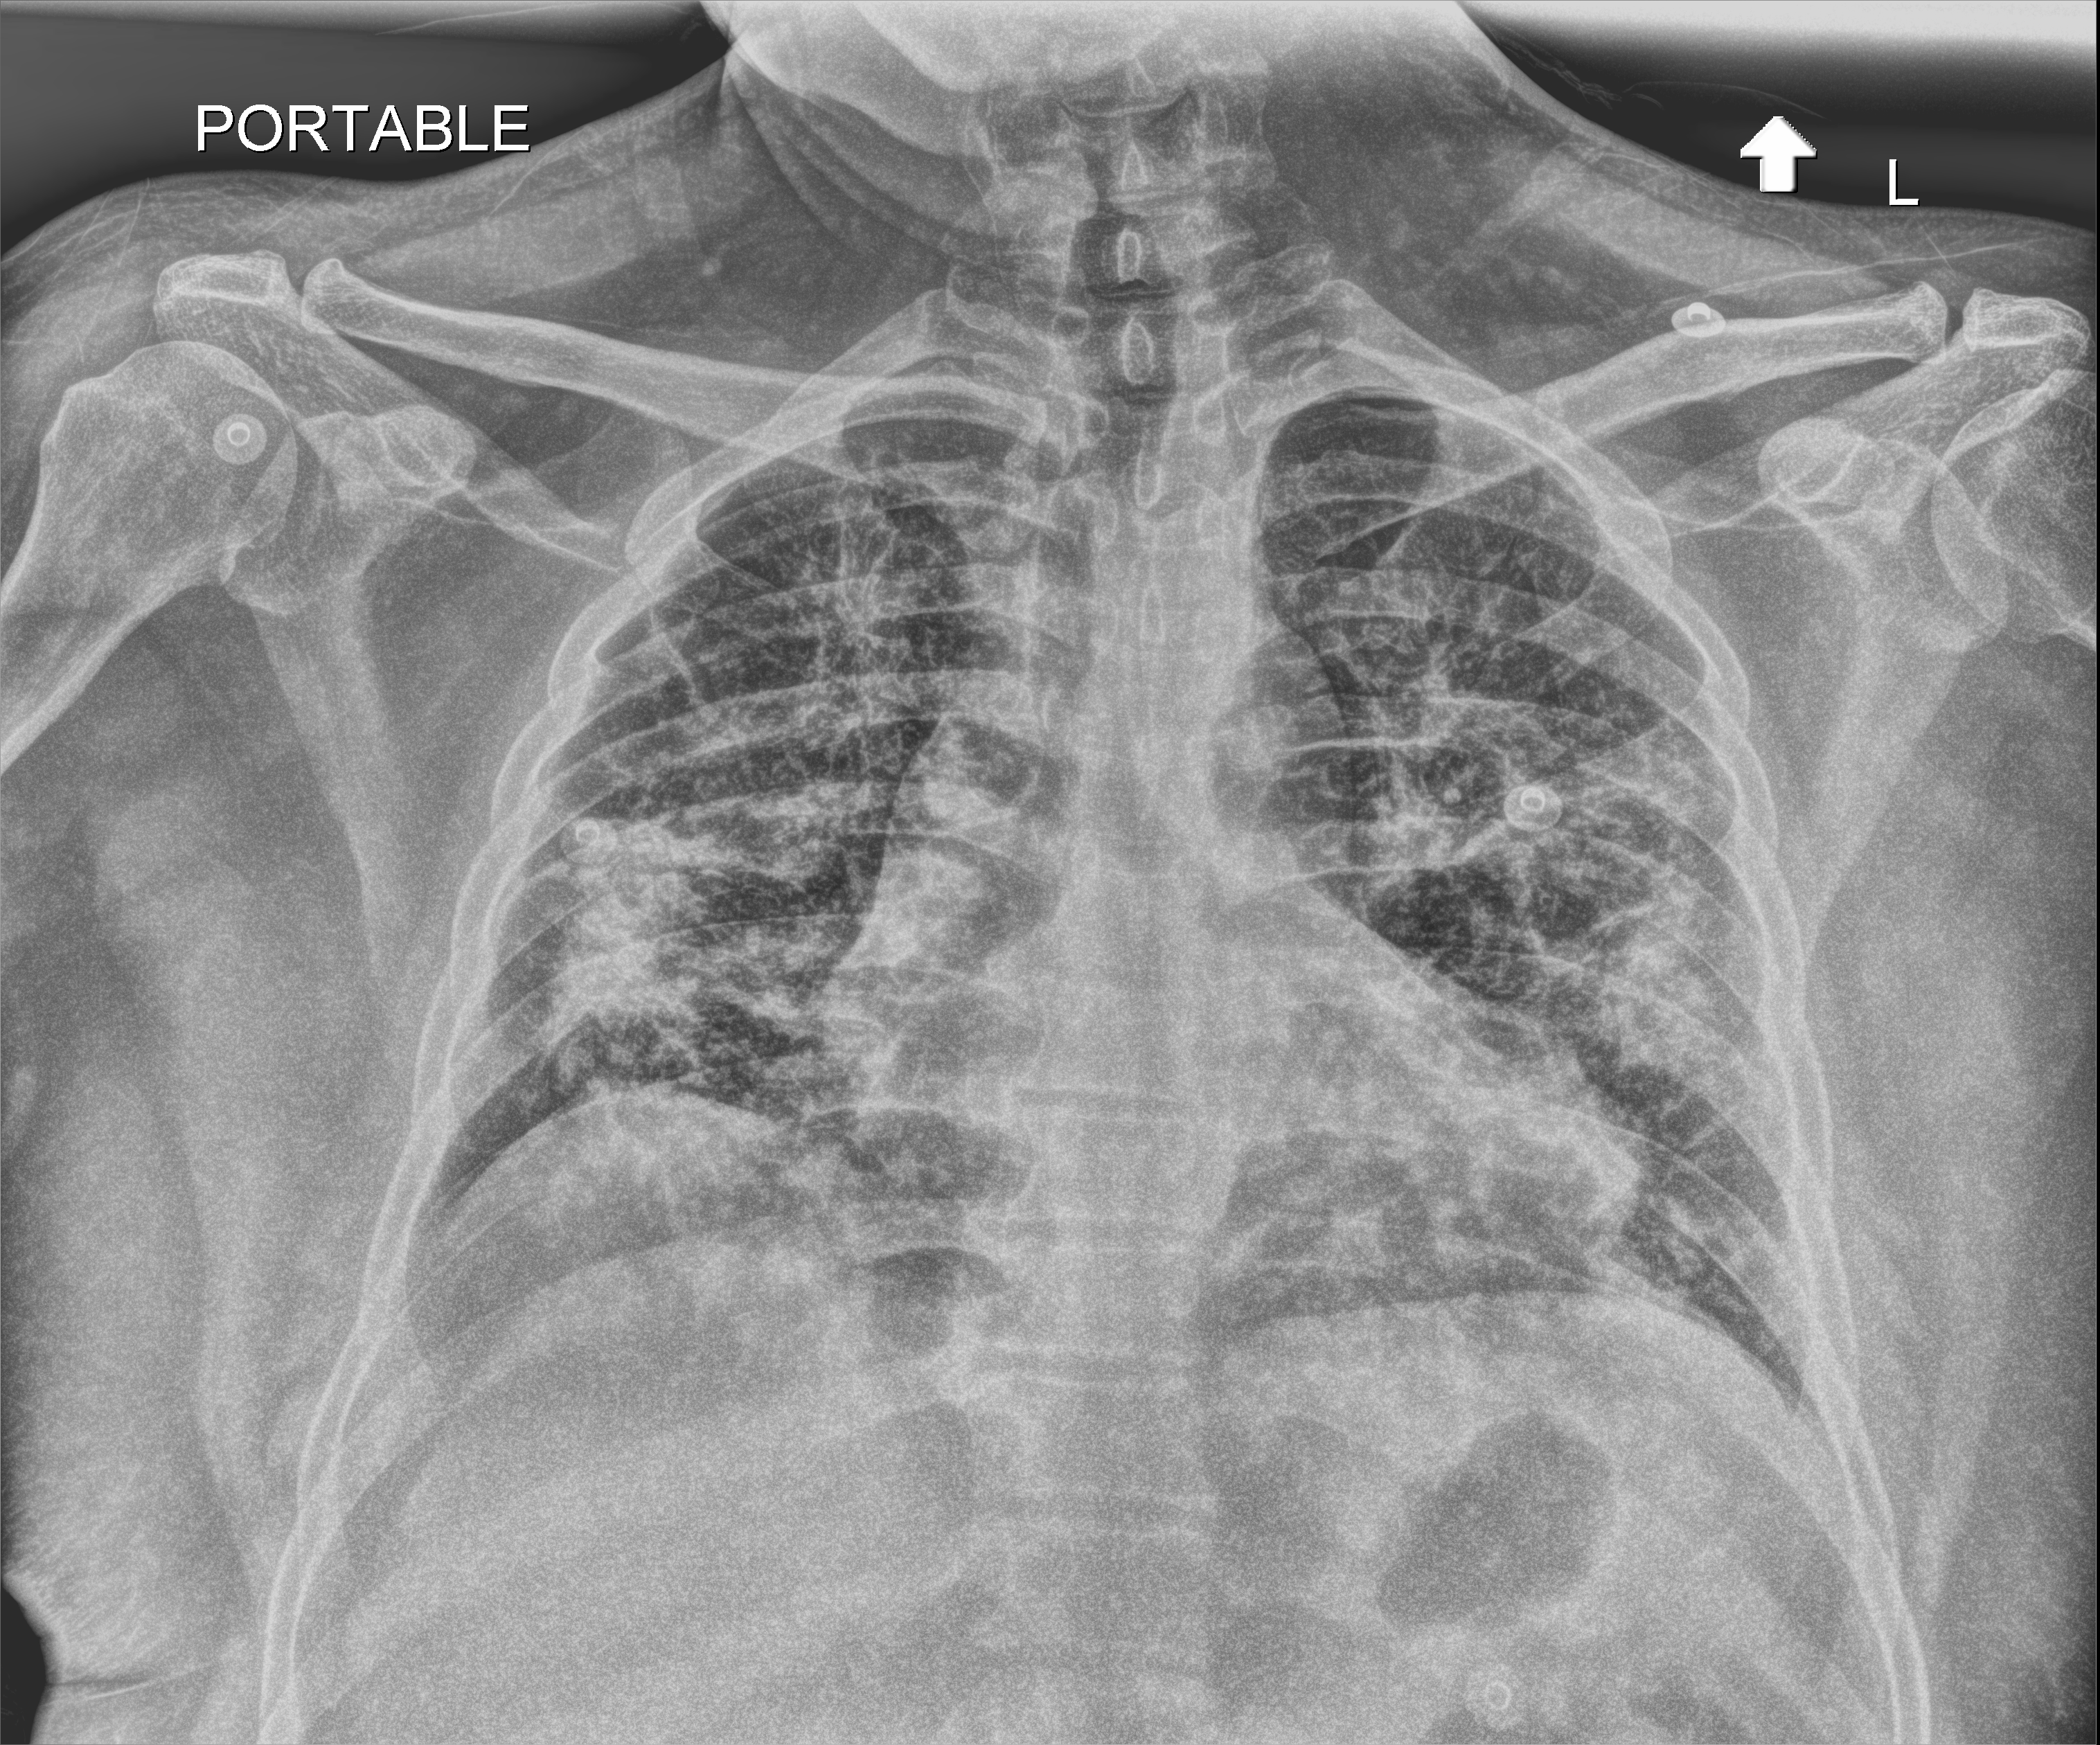
Chest X-ray, anteroposterior (AP) projection. Patient hospitalised with COVID-19; male, aged 18–59 years.
Hospital-stay facts (about this admission, not read from this image; timing relative to this image not recorded):
- mechanically ventilated during this hospital stay: no
- admitted to intensive care during this hospital stay: no
- length of hospital stay: 5 days